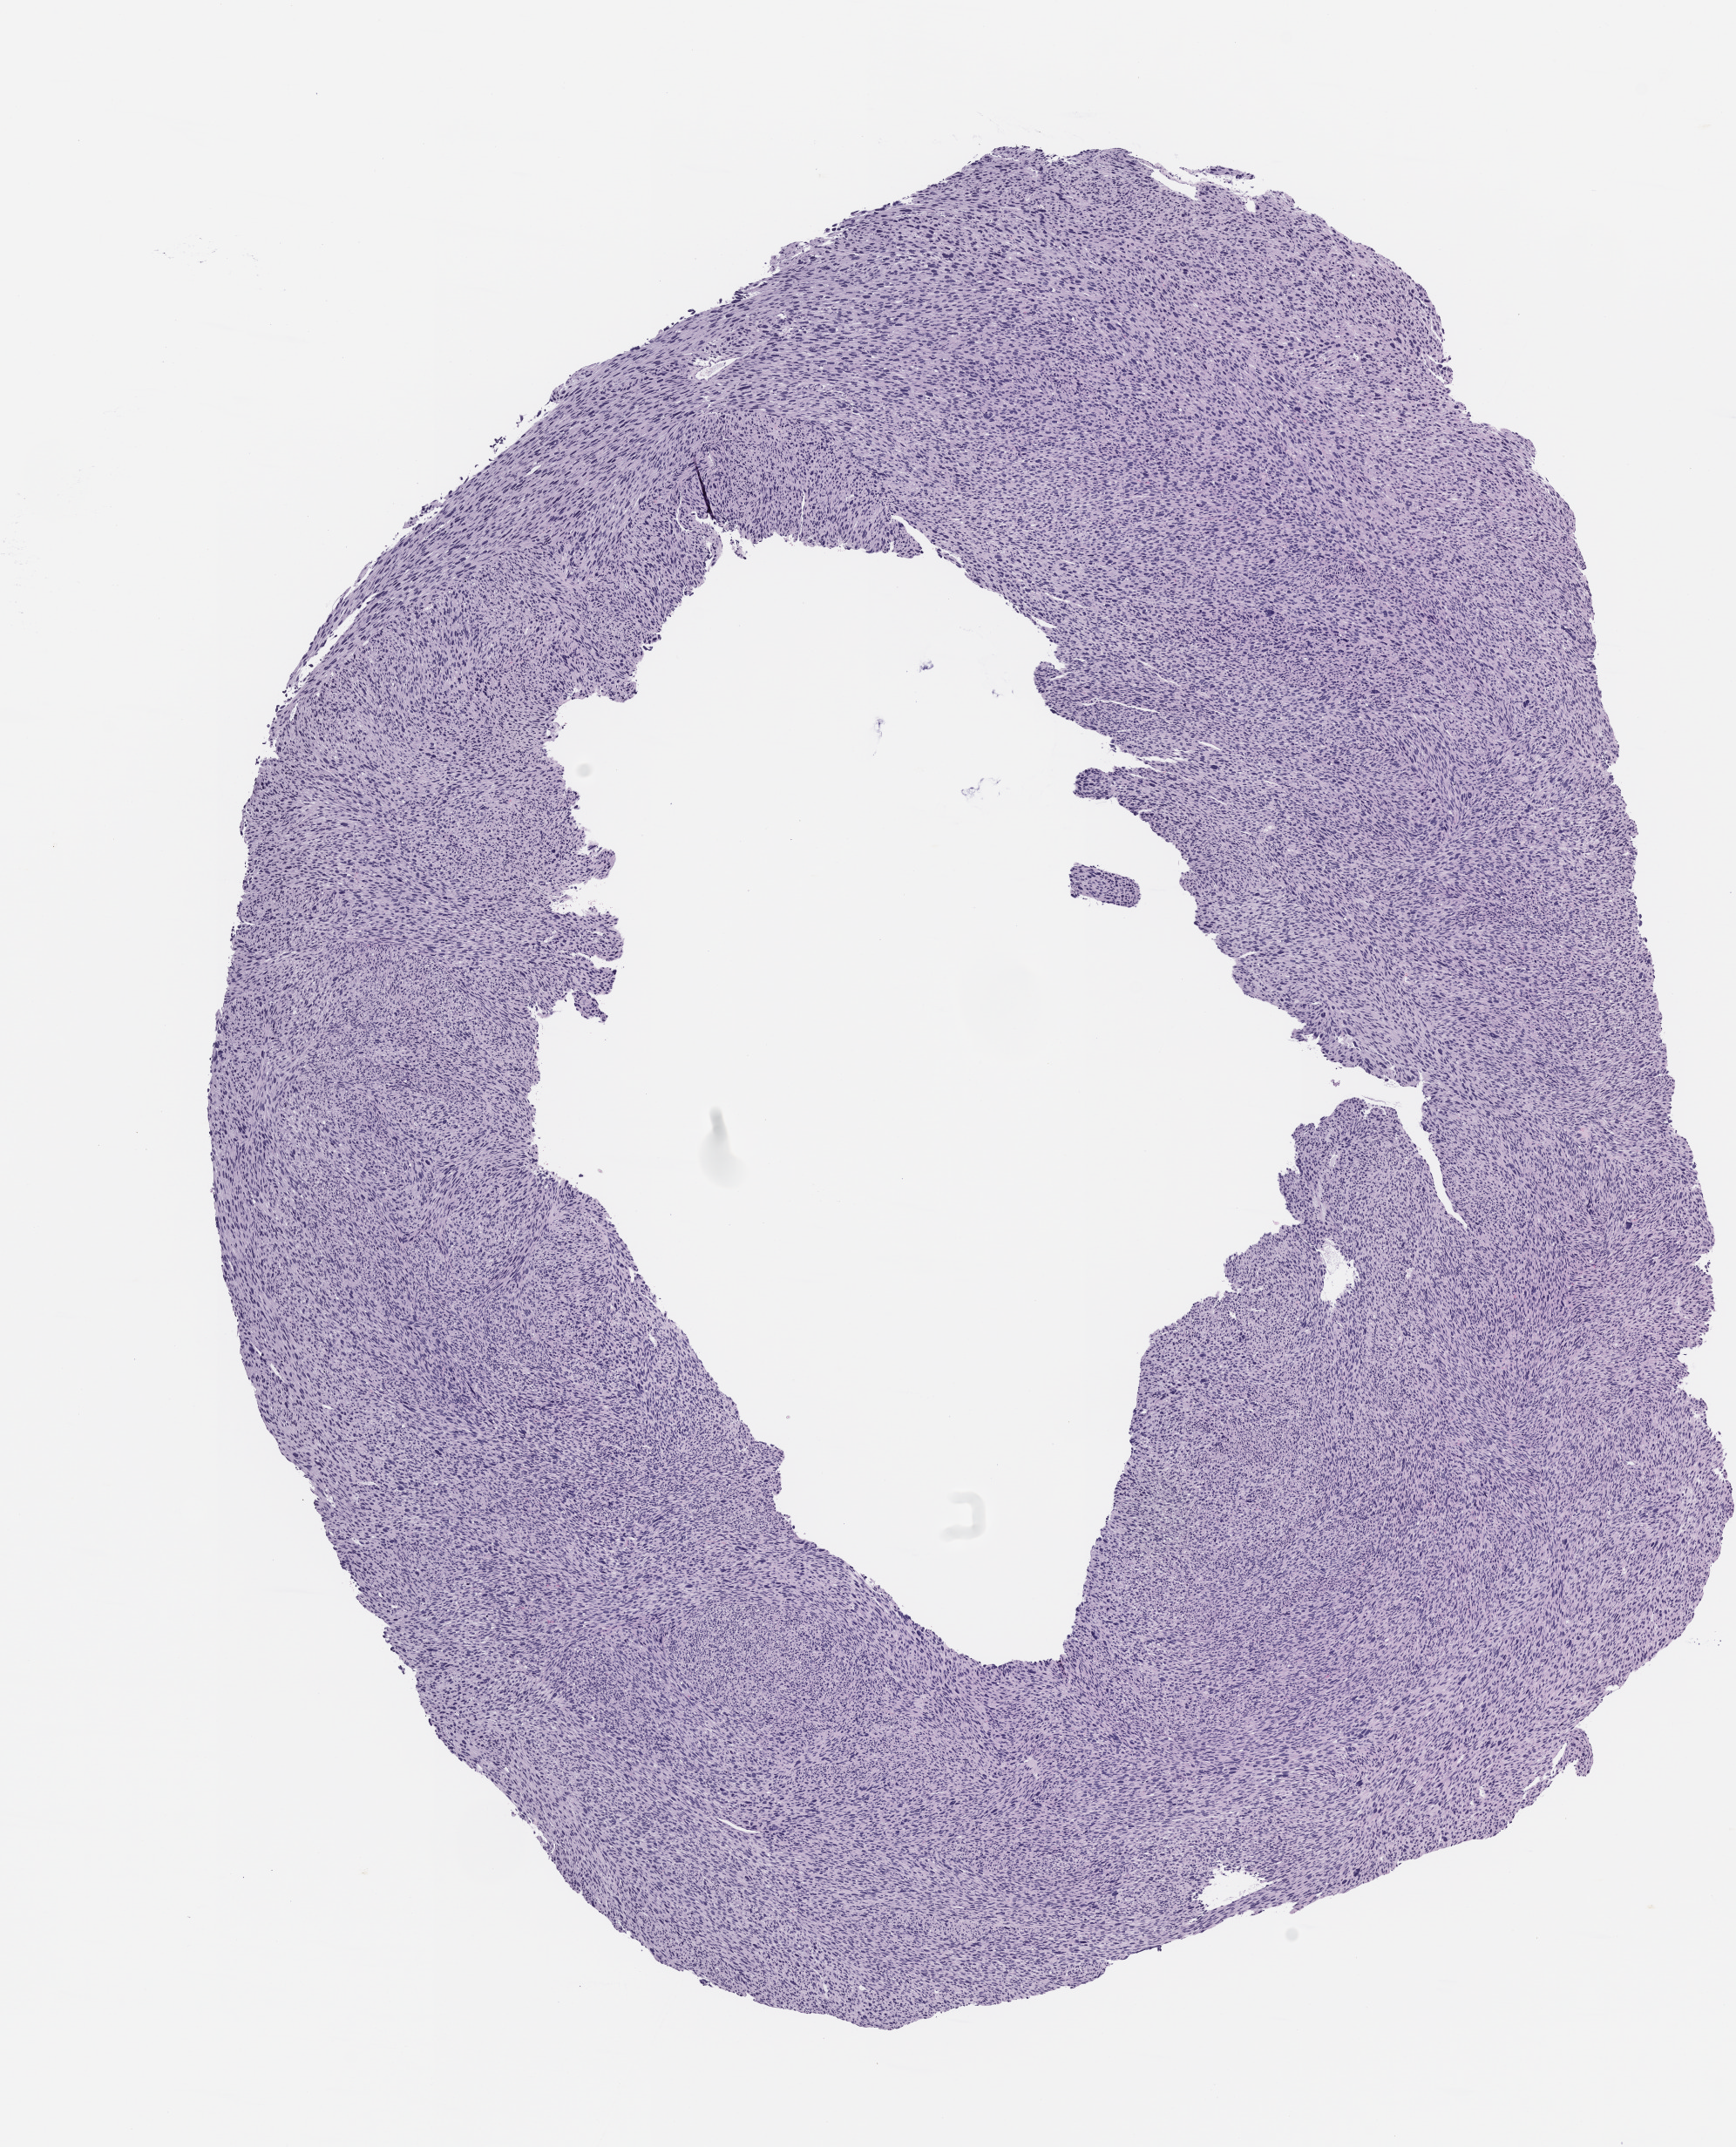
H&E whole-slide image of a patient-derived xenograft (PDX) tumor grown in a mouse, passage 2, whole scanned area (about 8.0 x 9.9 mm) shown as a low-resolution overview, FFPE section, tumor site category: musculoskeletal.
- originating patient diagnosis: Leiomyosarcoma